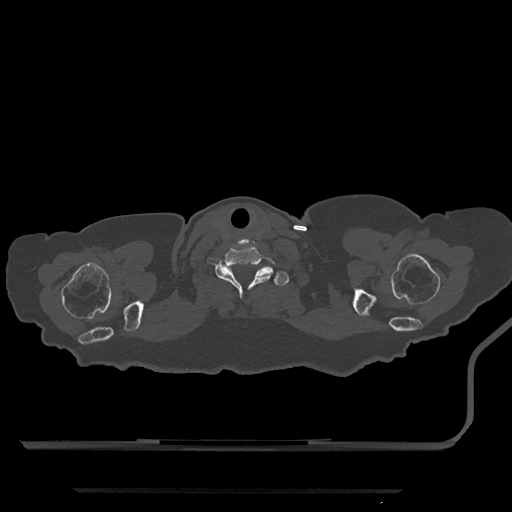
CT including the spine, one axial slice. Slice 733 of 797 in the series (ordered by position). Reconstruction kernel Br40s/3. Bone window (W 1800 / L 400 HU). 0.5 mm slice thickness. 512 × 512 image matrix. Female patient, age 51 years. Case-level facts recorded for this patient, not image findings: primary cancer: neuro.
Structures marked on this image (semi-automatically segmented with operator editing):
- T1 vertebra: bounding box <226,267,289,287> (left, top, right, bottom; pixels)